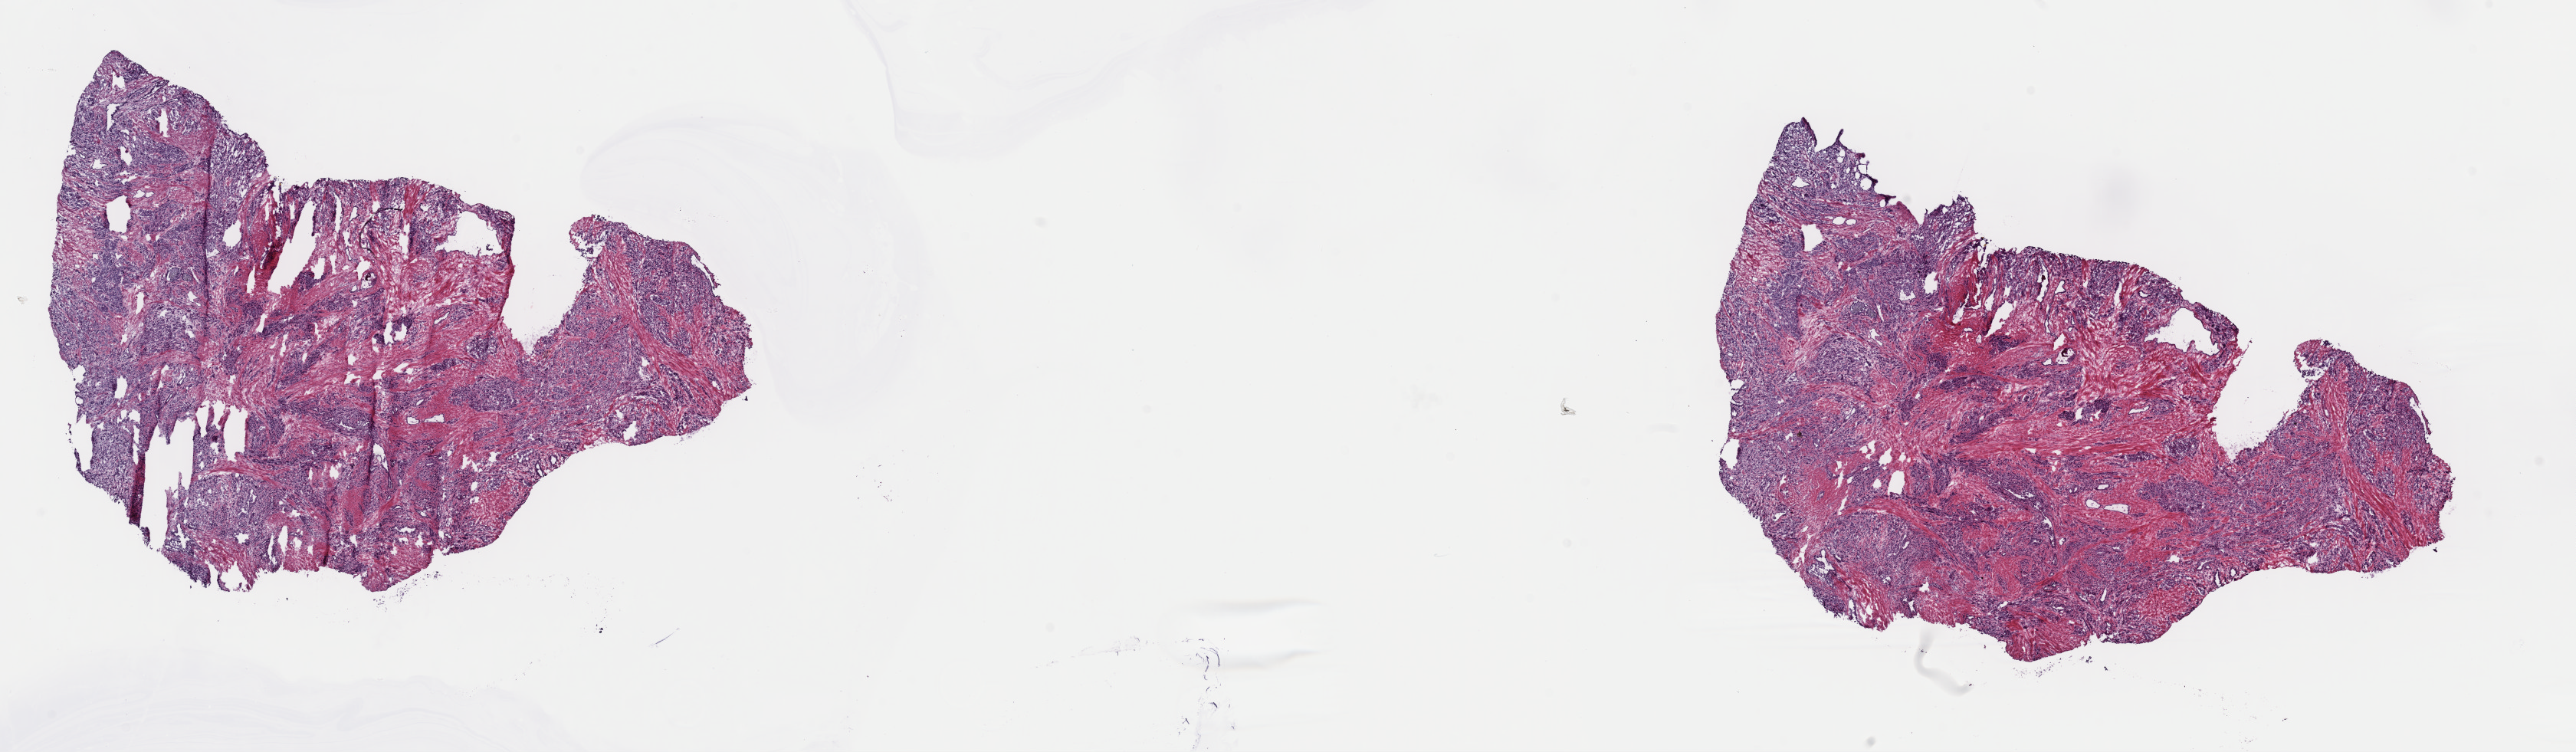
Digitized H&E-stained tissue section (whole slide) — a low-resolution overview of the entire scanned area, about 26.5 x 7.7 mm (from a 40x scan). Frozen section from the top of the tissue portion. Prostate, primary tumour sample. Male patient; age at initial diagnosis 62 years. Gleason score: 9 (5+4). Pathologist review of this section (percent, as recorded): tumour cells 95%, tumour nuclei 92%, normal cells 5%, stromal cells 0%, necrosis 0%. Infiltration values recorded for this section: lymphocyte infiltration 0%, monocyte infiltration 0%, neutrophil infiltration 0%.
Diagnosis: Acinar cell carcinoma.